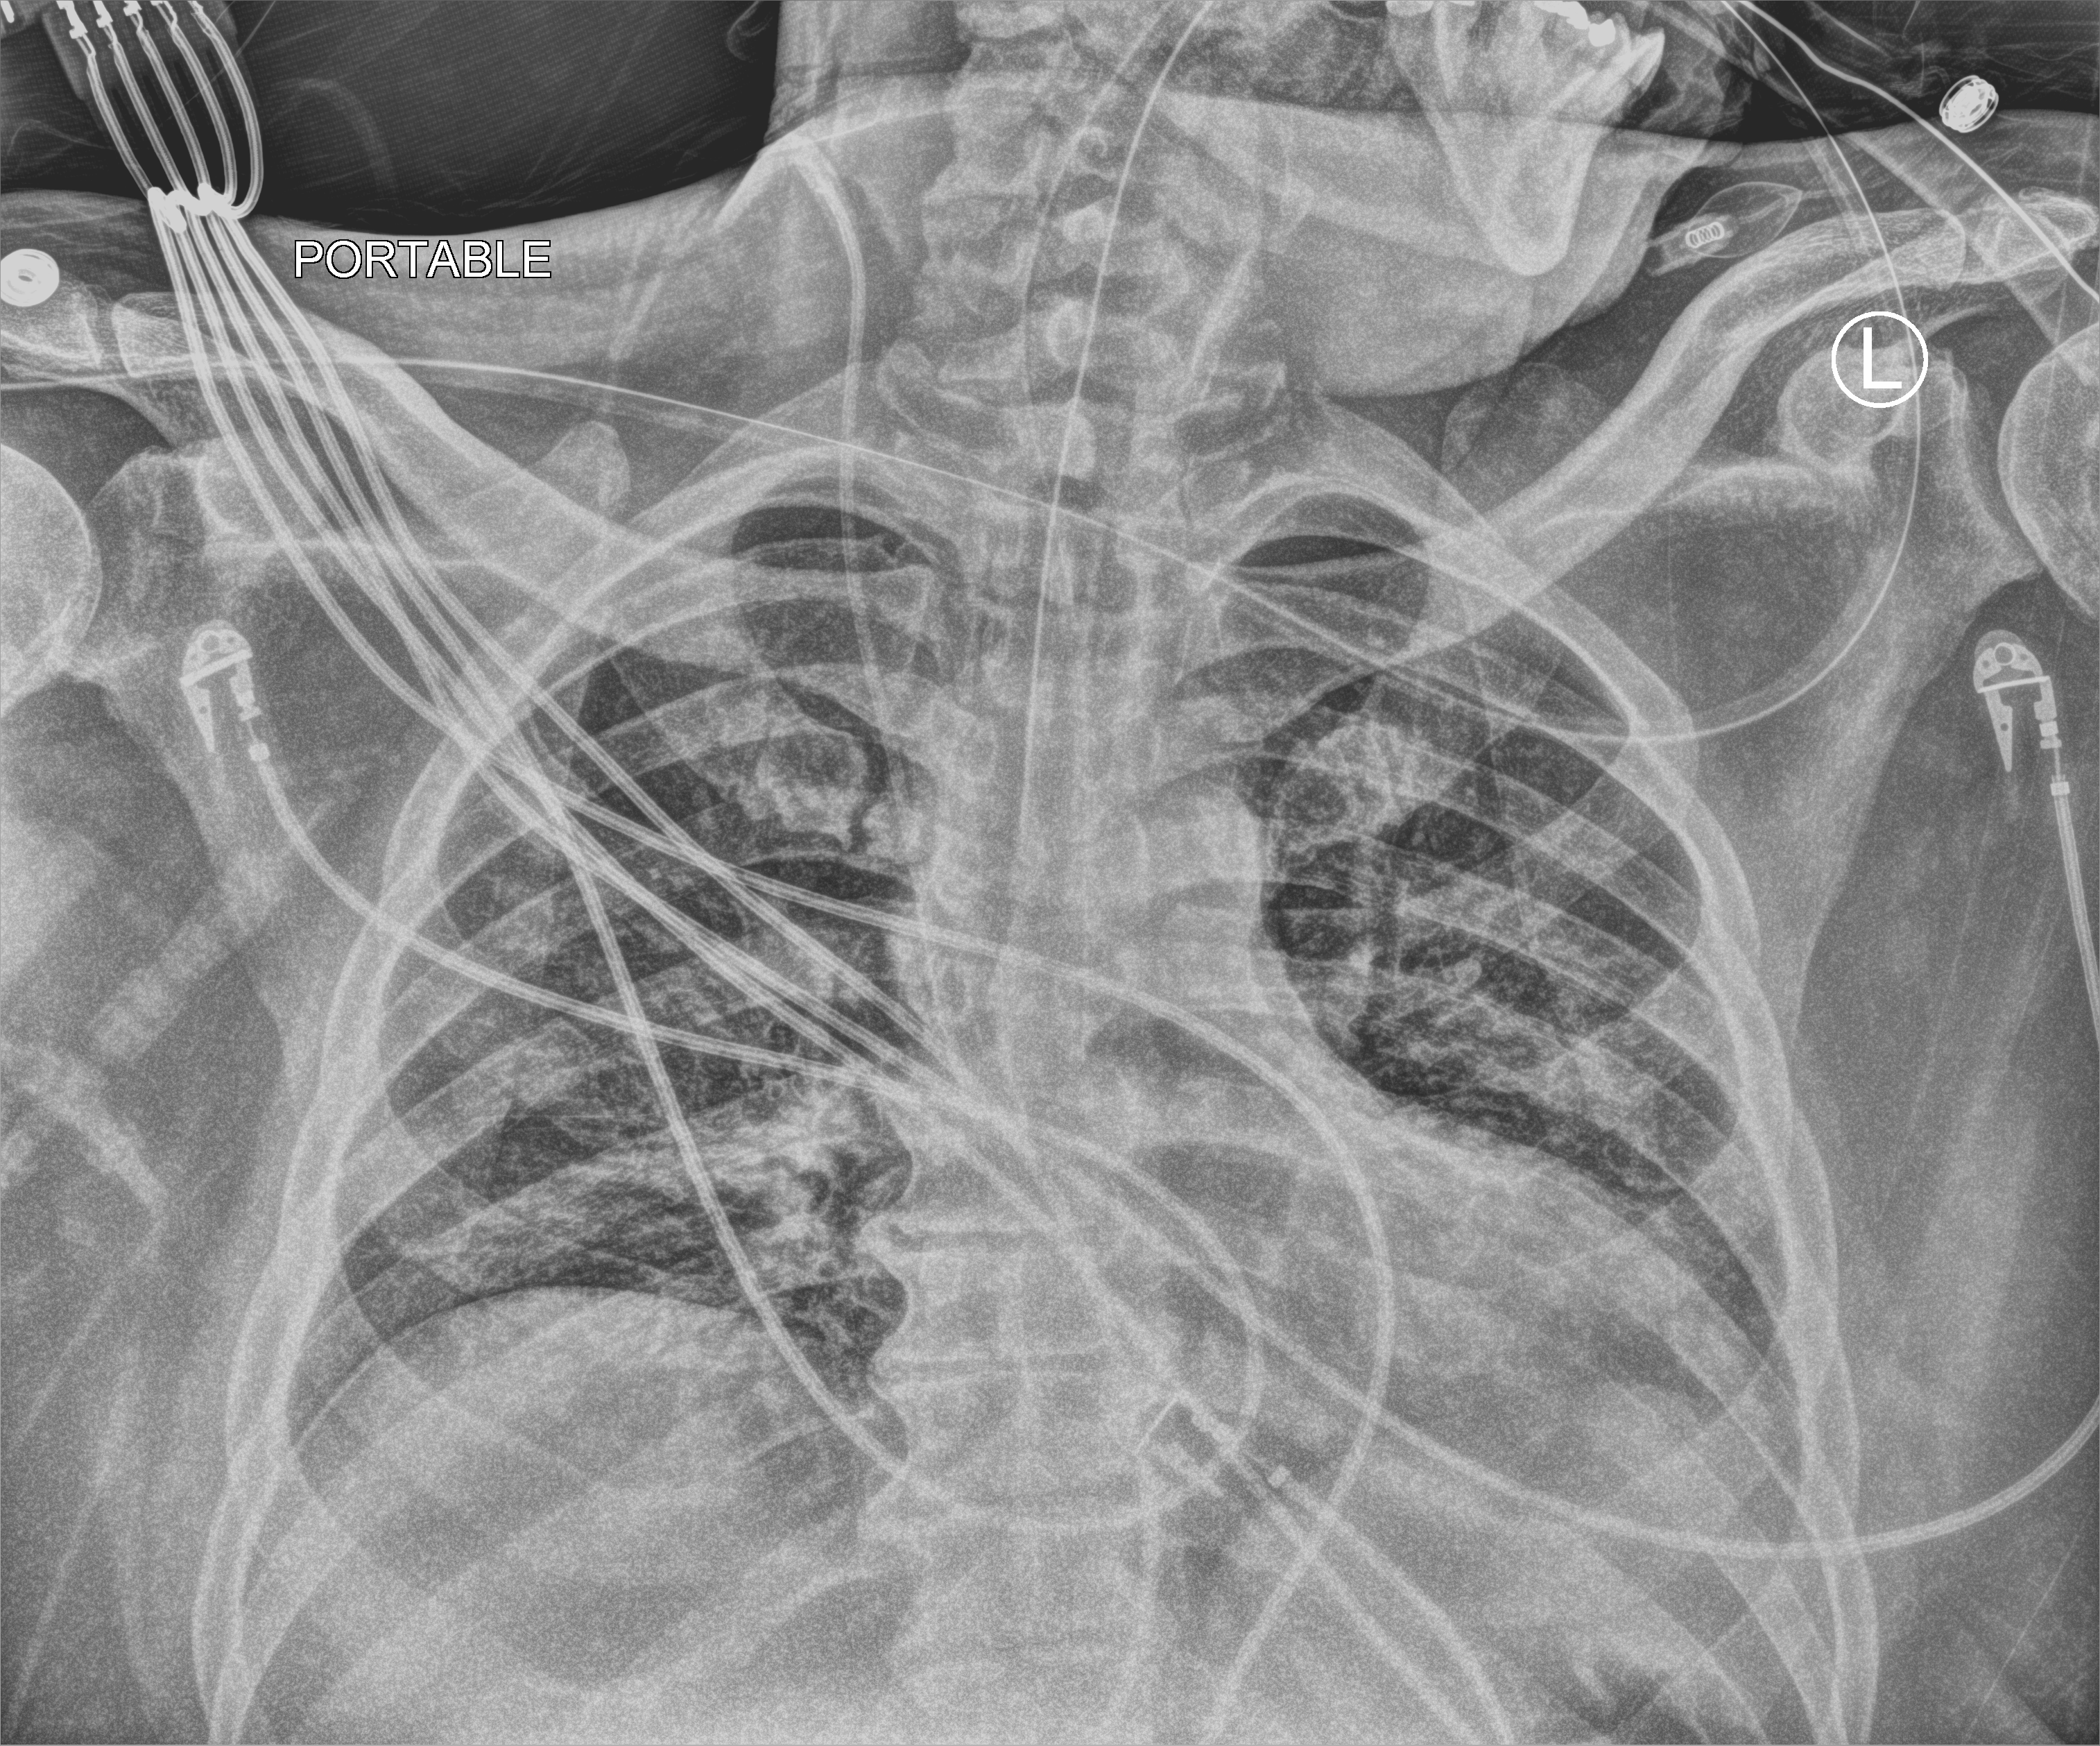
Bedside chest radiograph (computed radiography). Male patient hospitalised with COVID-19, age 18–59 years.
Admission-level facts for this patient (not findings on this image; timing relative to this image not recorded):
- admitted to intensive care during this hospital stay: yes